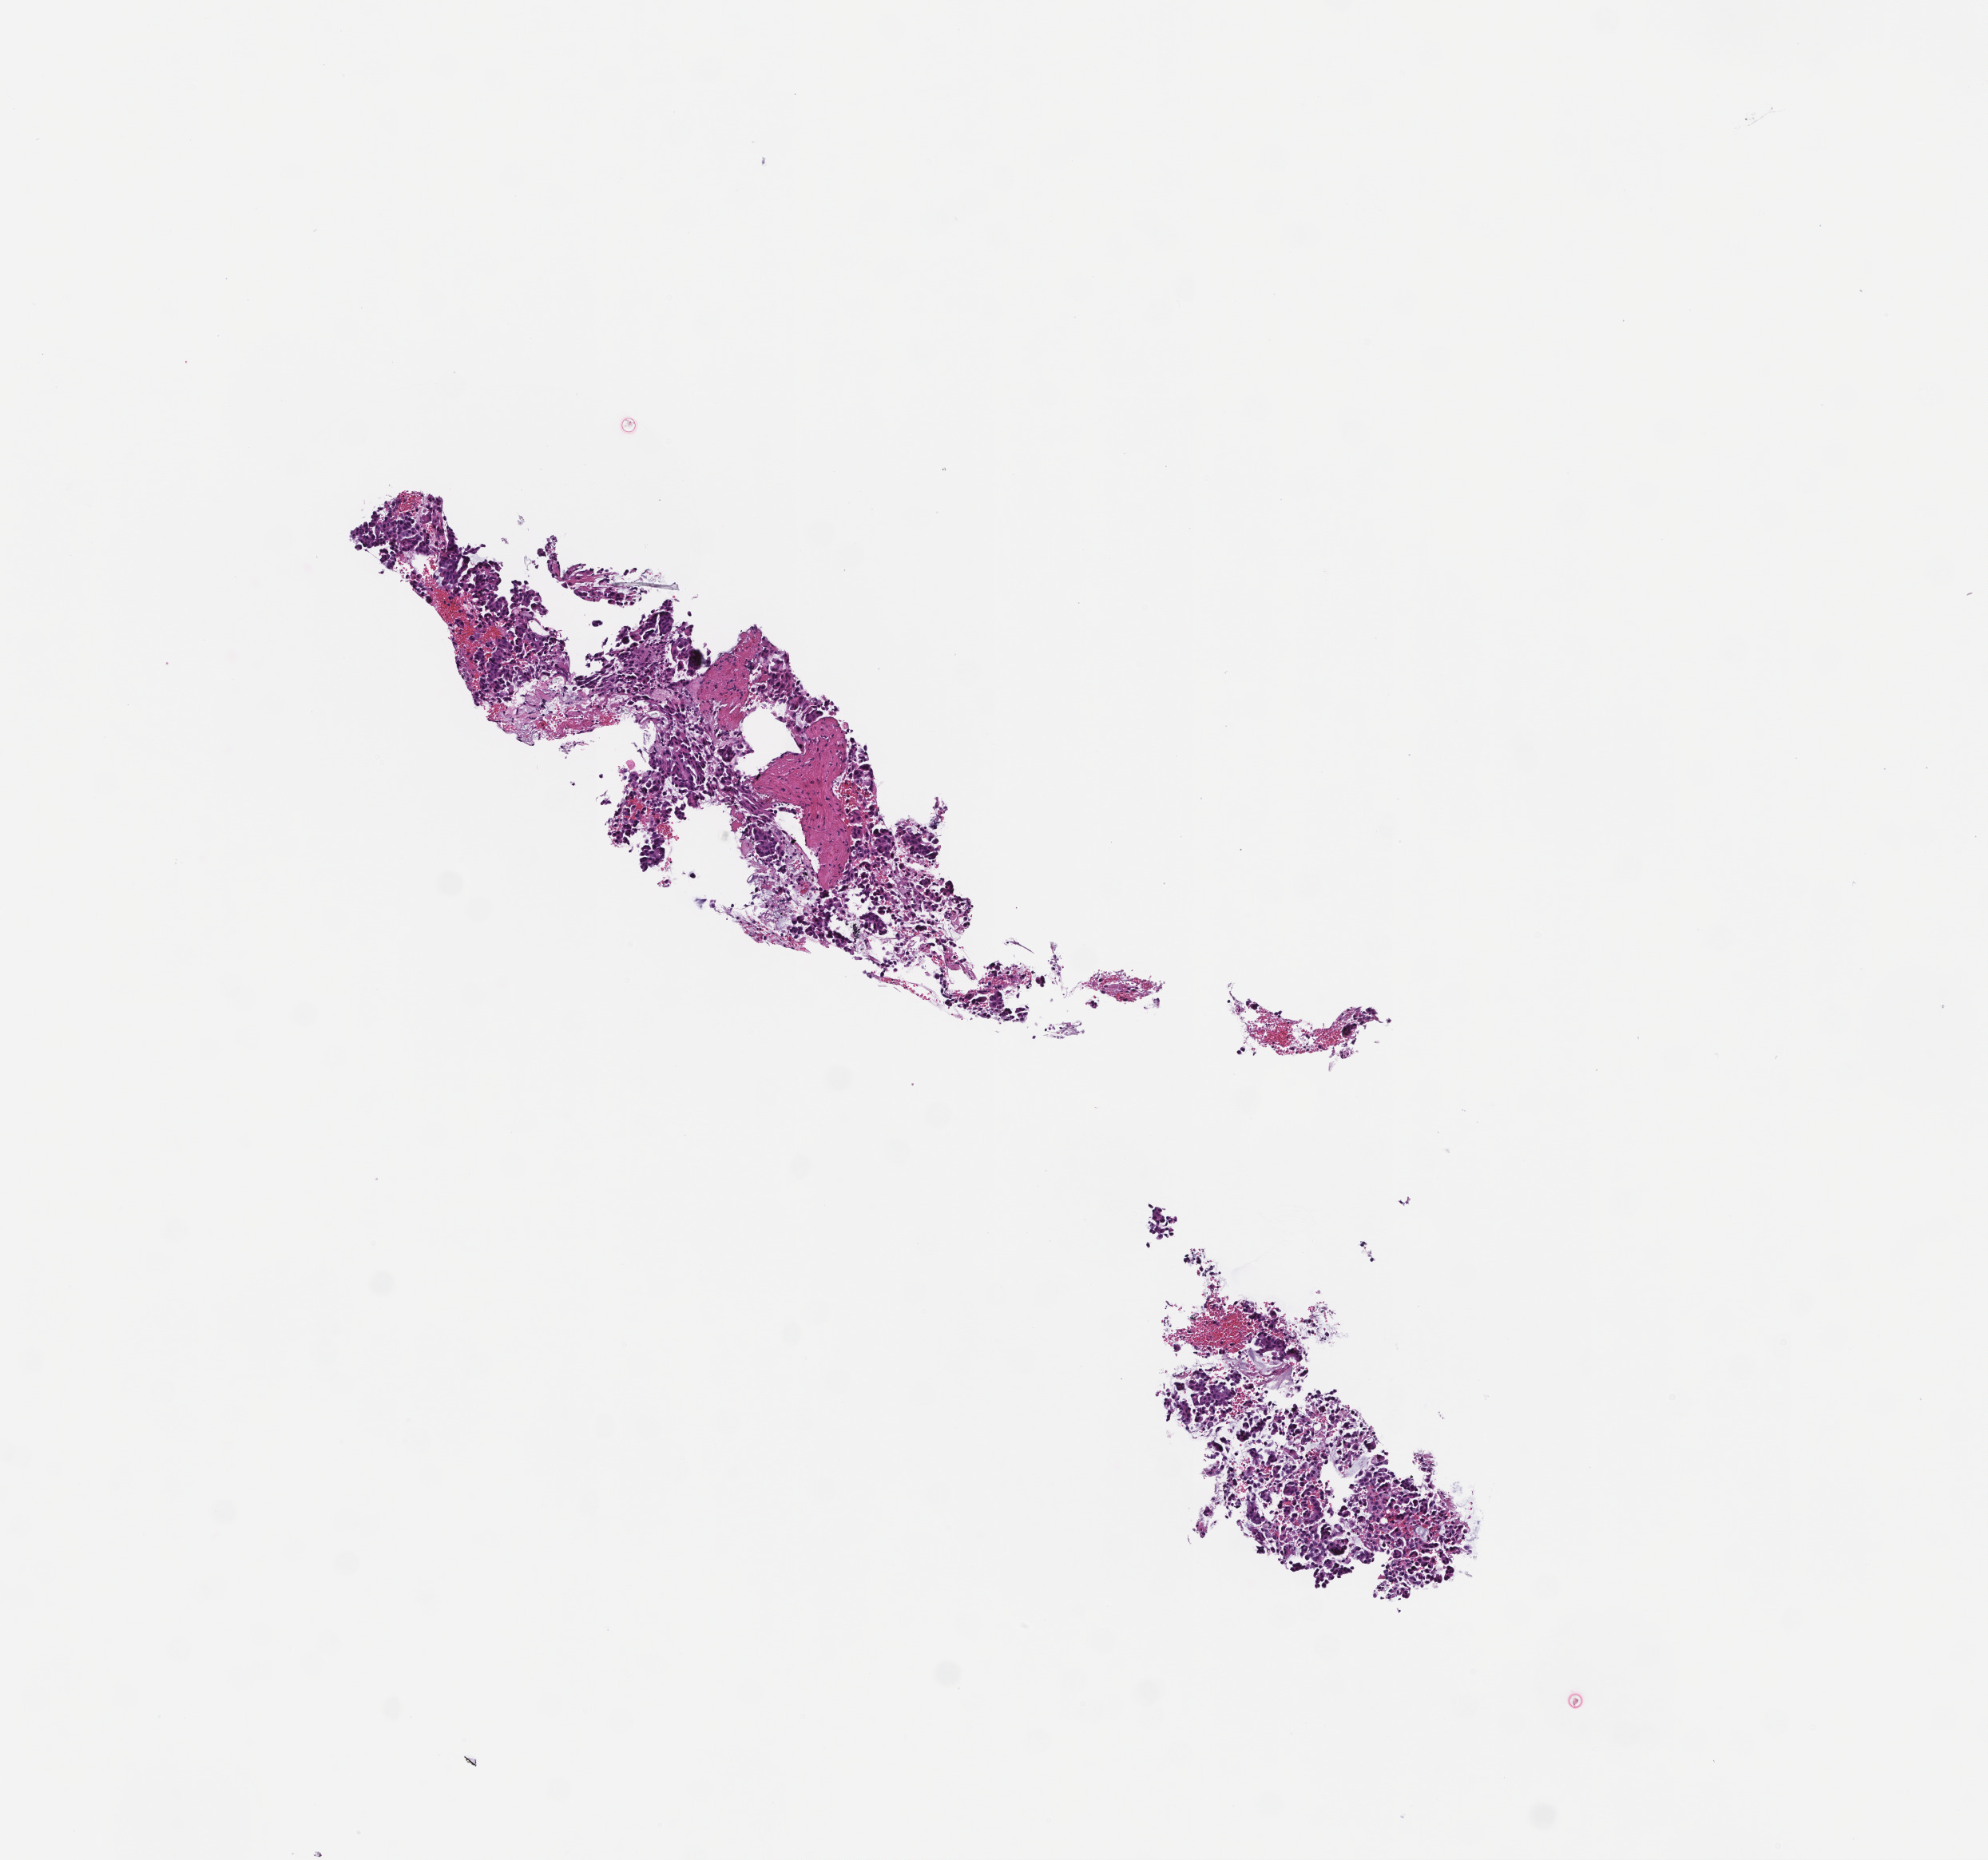
Hematoxylin and eosin (H&E) whole-slide image, low-resolution overview of the scanned area, about 5.0 x 4.7 mm; formalin-fixed paraffin-embedded section; site: lung. Patient: male.
This section: primary tumor. Diagnosis: Non-Small Cell Lung Carcinoma.